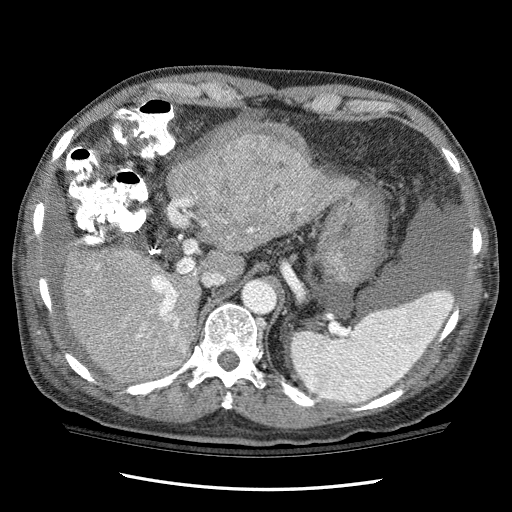
Contrast-enhanced abdominal CT (liver protocol), one axial slice; position 74 of 114 along the scan axis; one of 3 acquisitions stored at this slice position; soft-tissue window (W 400 / L 40 HU); 512 × 512 image matrix, field of view 360 × 360 mm. From the clinical record (not read from this slice): diagnosis: hepatocellular carcinoma (patient treated with transarterial chemoembolisation; whether this scan precedes or follows treatment is not stated here); TNM stage (as recorded): Stage-I; Child-Pugh class: C; tumour differentiation: well differentiated.
Outlined on this slice (semi-automatically segmented with operator editing):
- liver parenchyma outside the tumour (the mass and vessels are separate outlines, so this box may not span the whole liver): bounding box [x1, y1, x2, y2] px = [62, 157, 348, 382]
- mass: [217, 119, 309, 194]
- liver vessels: [96, 209, 301, 352]